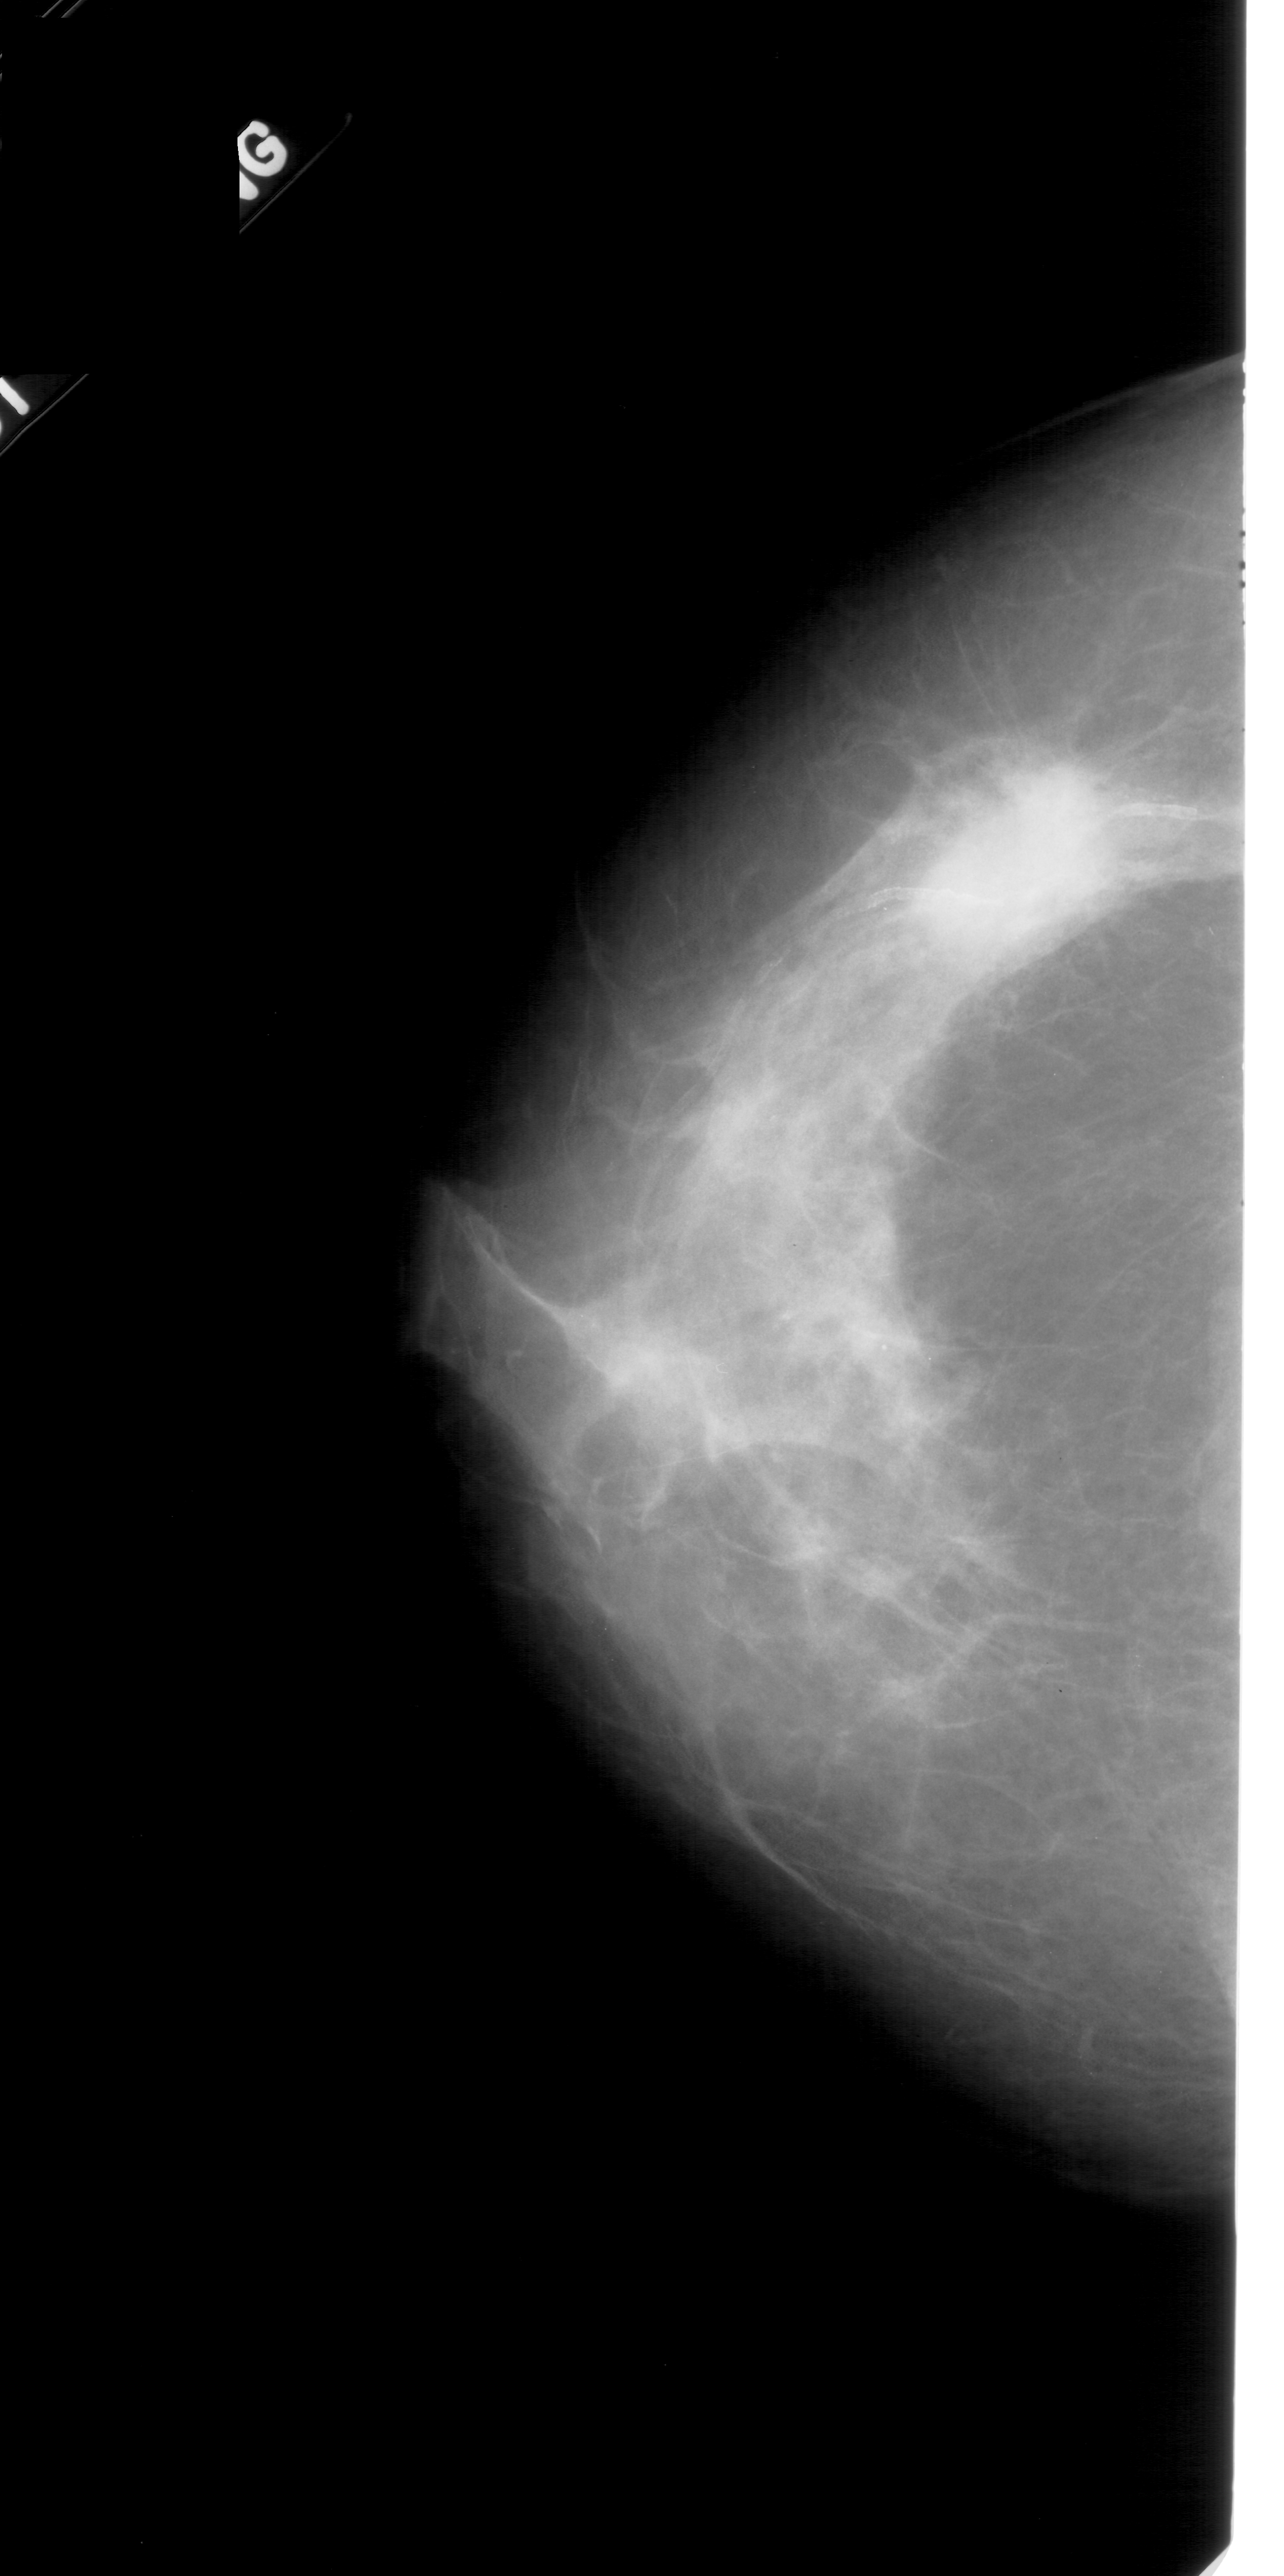
Digitized screen-film mammogram, left breast, CC view, BI-RADS breast density category 2 (scale 1–4).
Marked abnormality: mass, shape oval, margins ill defined; BI-RADS assessment category 4; subtlety rating 4 on a 1 (subtle) to 5 (obvious) scale; pathology (as recorded): malignant.